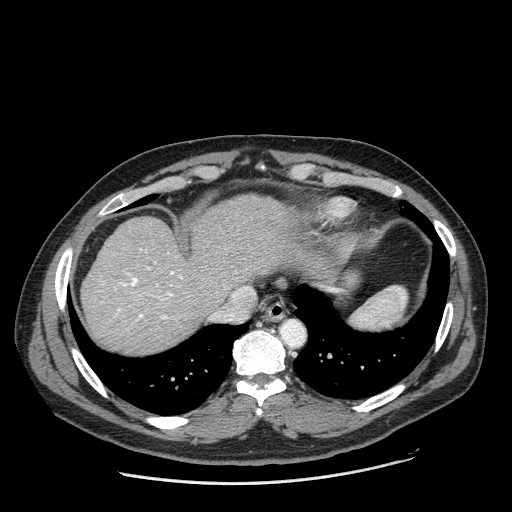
Contrast-enhanced abdominal CT (liver protocol), one axial slice; reconstruction kernel STANDARD; 120 kVp; one of 2 acquisitions stored at this slice position; soft-tissue window (W 400 / L 40 HU); 2.5 mm slice thickness; 512 × 512 image matrix, field of view 400 × 400 mm. From the clinical record (not read from this slice): diagnosis: hepatocellular carcinoma (patient treated with transarterial chemoembolisation; whether this scan precedes or follows treatment is not stated here); TNM stage (as recorded): Stage-II; Child-Pugh class: A; tumour differentiation: moderately differentiated; tumour nodularity: multinodular.
Outlined on this slice (semi-automatically segmented with operator editing):
- abdominal aorta: bounding box (x1, y1, x2, y2) in pixels: (282, 321, 303, 344)
- liver parenchyma outside the tumour (the mass and vessels are separate outlines, so this box may not span the whole liver): (82, 194, 309, 352)
- liver vessels: (114, 249, 183, 321)